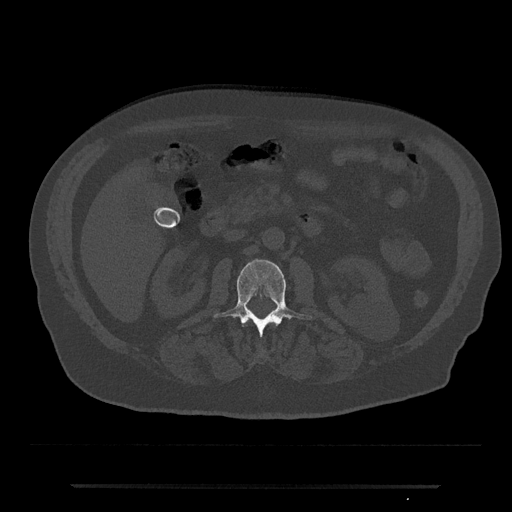
CT including the spine, one axial slice. Position 475 of 797 along the scan axis. Bone window (W 1800 / L 400 HU). 0.5 mm slice thickness. 512 × 512 image matrix, field of view 434 × 434 mm. Male patient, age 80 years. From the clinical record (not read from this slice): primary cancer: prostate.
Structures marked on this image (semi-automatically segmented with operator editing):
- L2 vertebra: bounding box (x1, y1, x2, y2) in pixels: (214, 259, 312, 338)